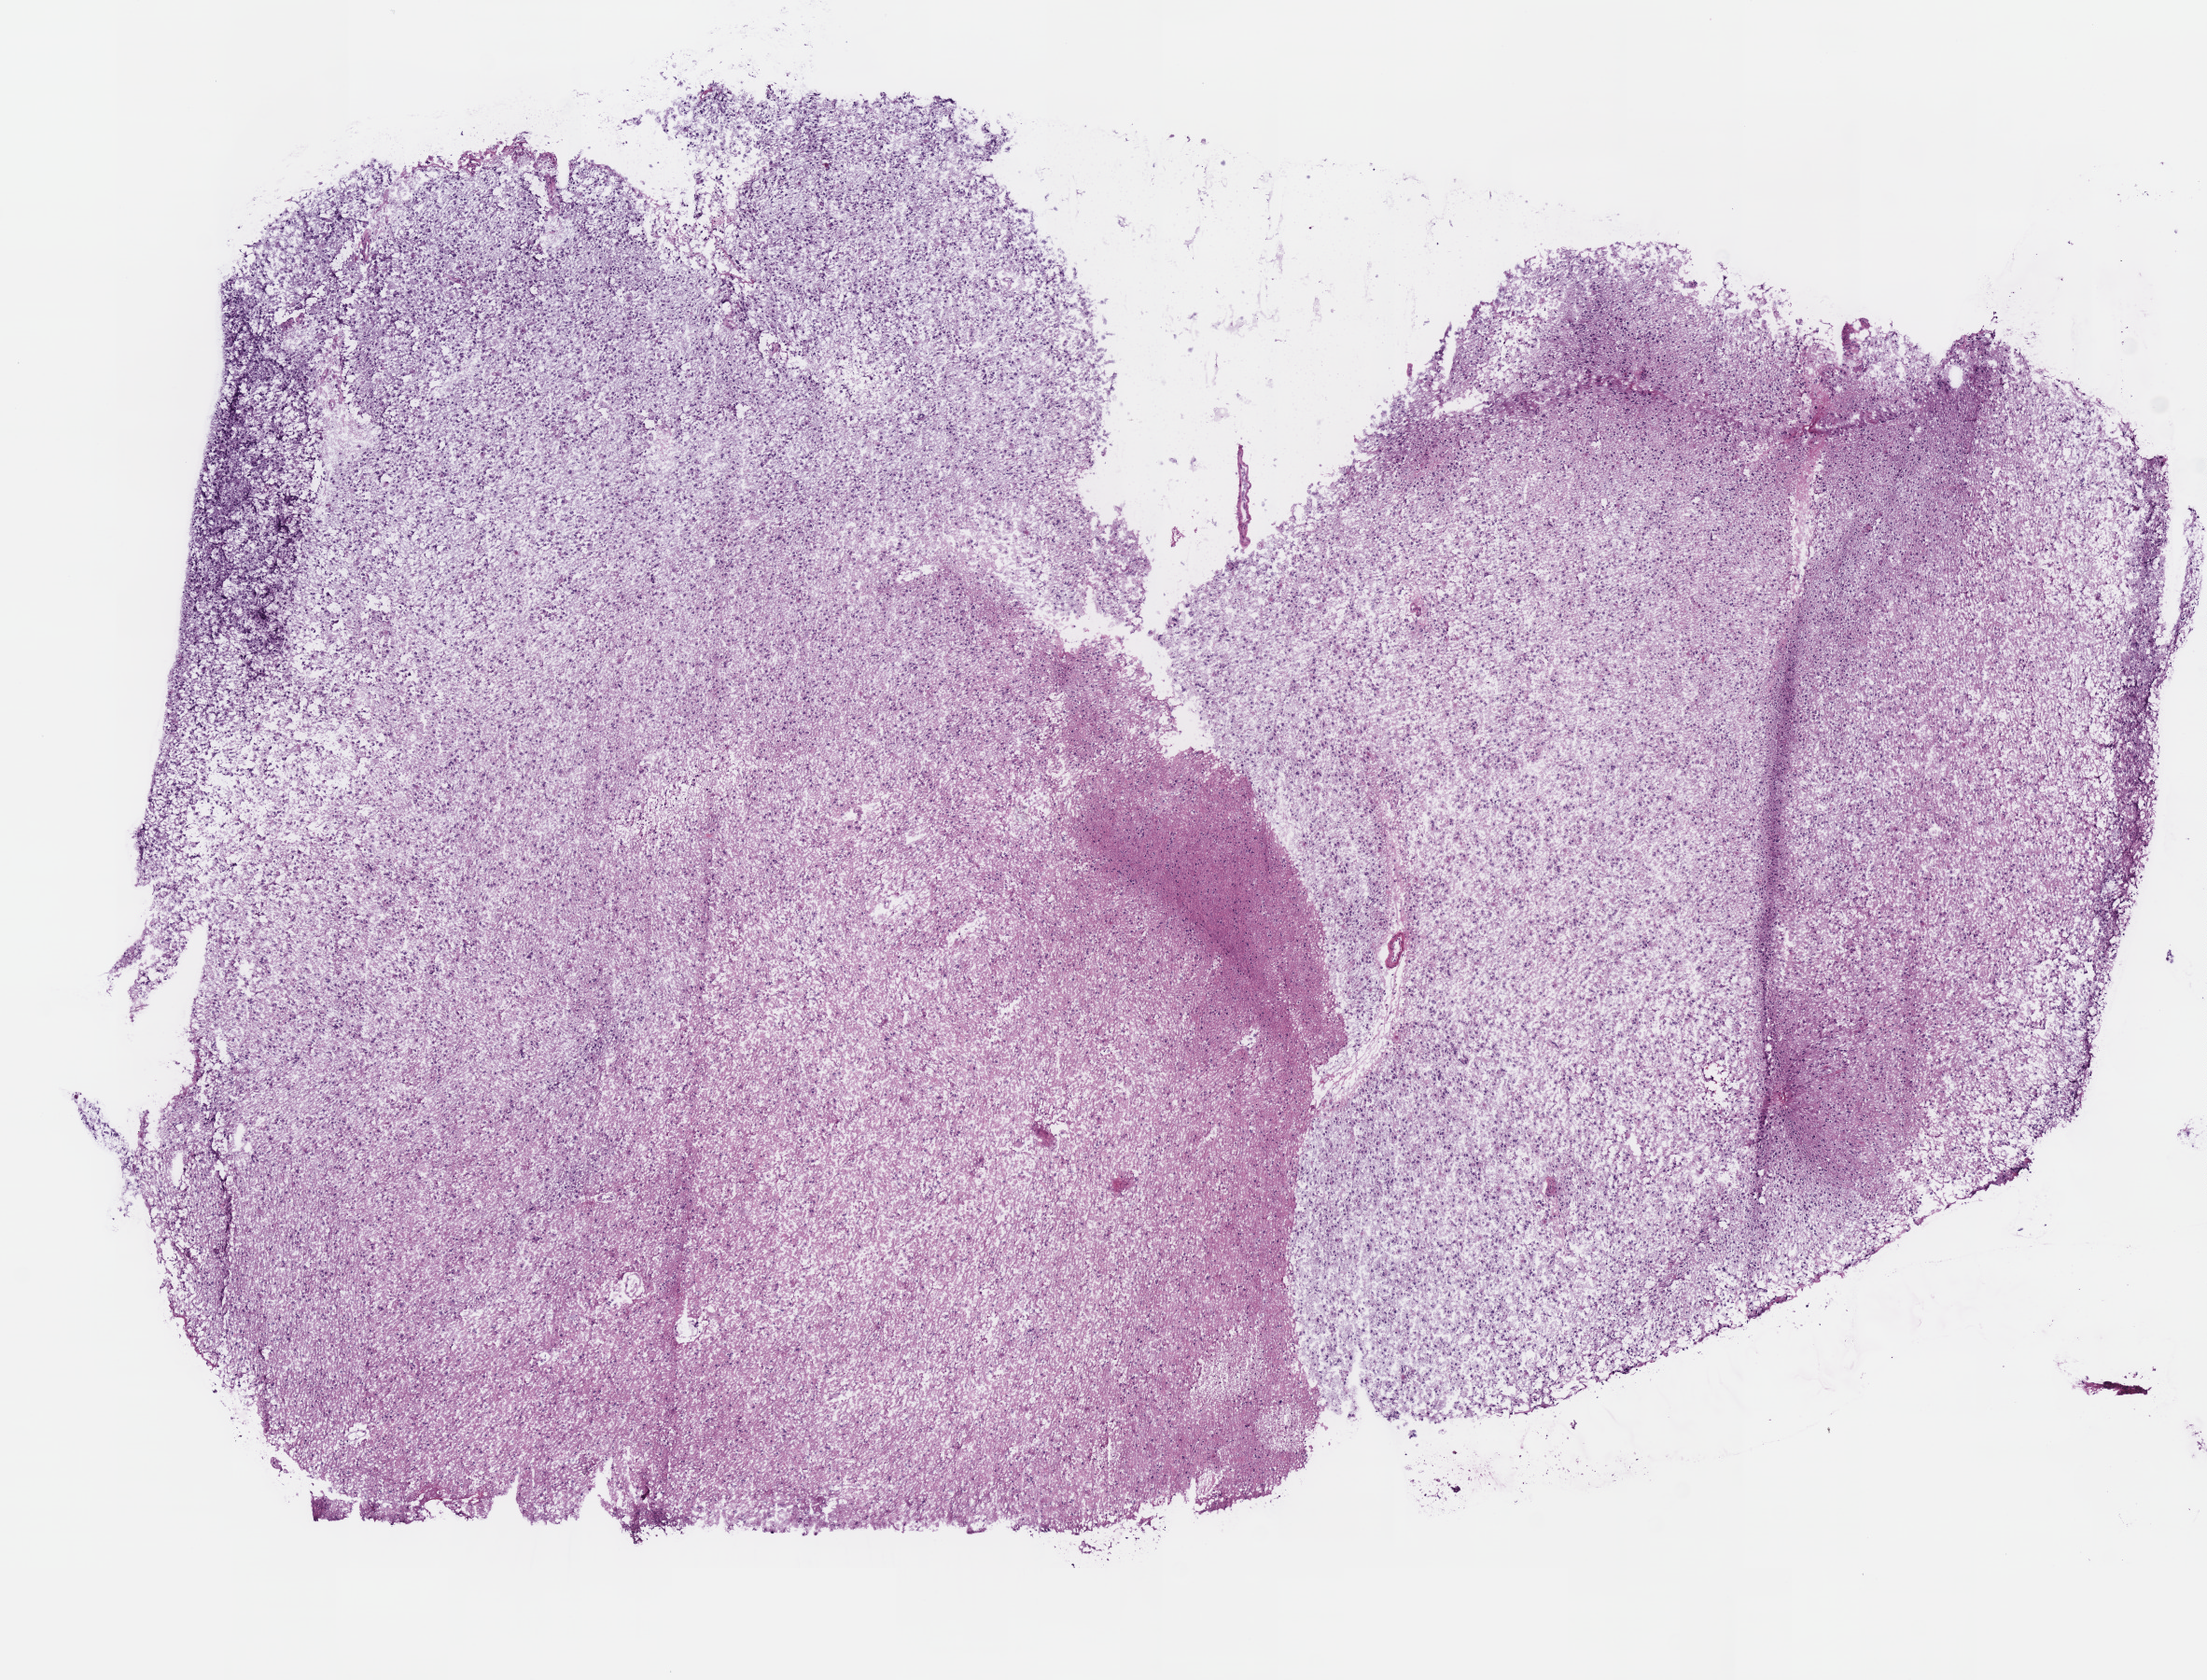
Hematoxylin and eosin (H&E) stained whole-slide image — low-resolution overview of the scanned area, about 9.3 x 7.1 mm. Frozen section from the top of the tissue portion. Primary tumour sample from the brain. Patient: female, age at initial diagnosis 44 years. Histologic grade: G2 (moderately differentiated). Pathologist review of this section (percent, as recorded): tumour cells 100%, tumour nuclei 75%, normal cells 0%, stromal cells 0%, necrosis 0%.
Histologic diagnosis: Astrocytoma, NOS (cerebrum).